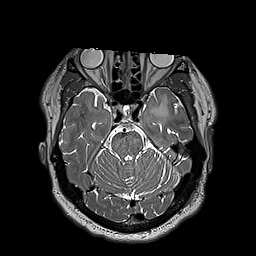
Brain MRI from a brain-tumour surgery series, one axial slice. 1 mm slice thickness. 256 × 256 image matrix, field of view 250 × 250 mm. Case-level facts recorded for this patient, not image findings: histopathology: Astrocytoma; WHO grade: 3; IDH mutation: yes; tumour location: Left Insular.
Annotated regions visible in this slice (manually delineated by an expert):
- tumour: bounding box (x1, y1, x2, y2) in pixels: (150, 97, 168, 120)